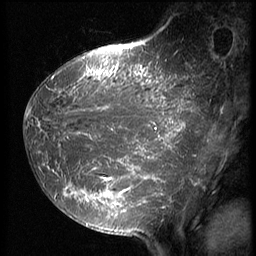
Breast MRI (dynamic contrast-enhanced), one sagittal slice. Slice 22 of 64 in the series (ordered by position). 3 images stored at this slice position (order not interpretable as contrast timing). 1.5 T. TE 4.2 ms, TR 9 ms. 2.5 mm slice thickness. 256 × 256 image matrix, field of view 180 × 180 mm. Female patient, age 39 years. From the clinical record (not read from this slice): setting: breast cancer imaged before/during neoadjuvant chemotherapy; receptor status: HER2-positive.
Annotated regions visible in this slice (semi-automatically segmented with operator editing):
- analysis volume of interest (the breast-tissue region the enhancement analysis was run in; not a lesion): box from (x=23, y=47) to (x=210, y=239) px
- tumour enhancement mask (voxels above the 140 % enhancement threshold inside the analysis volume of interest): (x=25, y=47)–(x=206, y=225)